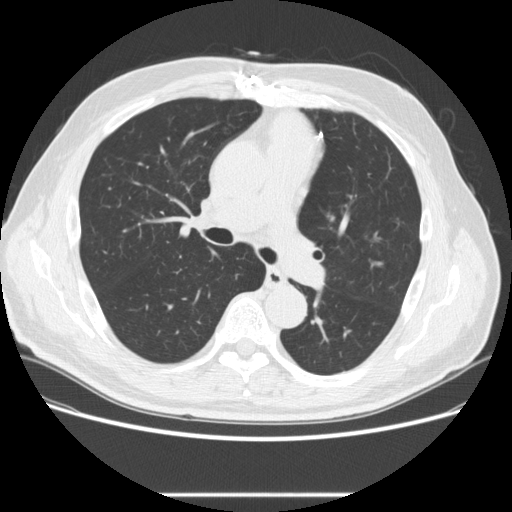
Chest CT (low-dose screening protocol), one axial image. Second annual screen. Lung window (W 1500 / L -600 HU). Standard (soft-tissue) reconstruction kernel (STANDARD). Slice 93 of 268 in the series. Male, age 66 years at enrolment.
Expert reader's lesion annotation, bounding box (x1, y1, x2, y2) in pixels: (318, 198, 350, 231). Screening reader's record for this exam (one nodule recorded; not confirmed to be the boxed lesion): non-calcified nodule or mass ≥4 mm, right lower lobe, 4 × 4 mm, smooth margins, soft tissue attenuation, pre-existing on the prior screen: yes; interval growth: no. Note: the box lies in the patient's left hemithorax on this image, whereas the reader's record names the right lung; they may be different findings. Later outcome: lung cancer diagnosed 449 days after this screen — squamous cell carcinoma, NOS, left upper lobe, poorly differentiated (G3), stage IA (AJCC 6th edition), 27 mm at pathology.